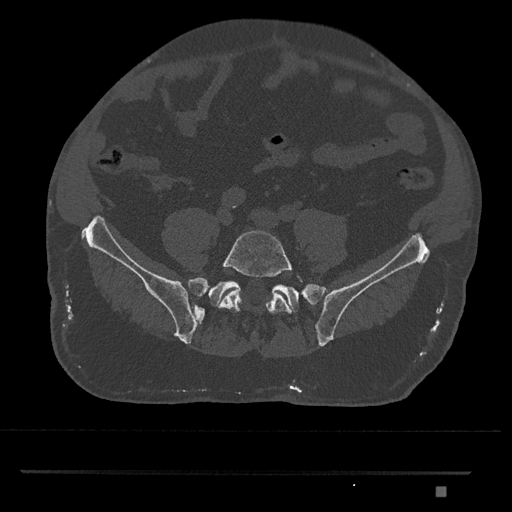
CT including the spine, one axial slice. Slice 540 of 1134 in the series (ordered by position). Reconstruction kernel Br40s/3. 120 kVp. Bone window (W 1800 / L 400 HU). 0.5 mm slice thickness. 512 × 512 image matrix, field of view 429 × 429 mm. Male patient, age 65 years. Case-level facts recorded for this patient, not image findings: primary cancer: prostate.
Annotated regions visible in this slice (semi-automatically segmented with operator editing):
- L5 vertebra: box from (x=219, y=229) to (x=303, y=314) px